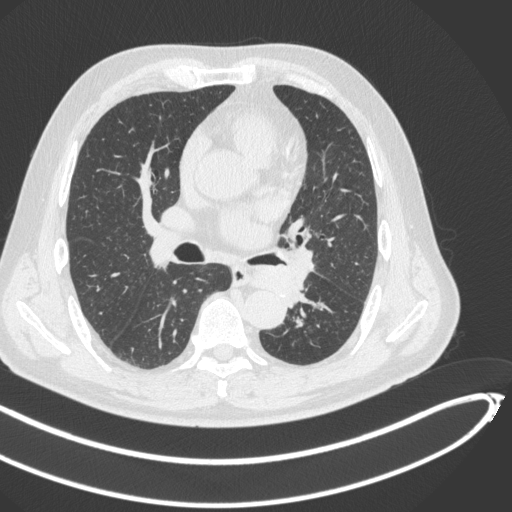
Chest CT, one axial slice; position 255 of 466 along the scan axis; reconstruction kernel B31f; 120 kVp; lung window (W 1500 / L -600 HU); 1 mm slice thickness; 512 × 512 image matrix, field of view 400 × 400 mm. Male patient, age 64 years. From the clinical record (not read from this slice): clinical TNM (as recorded): T1c N0 M0.
Annotated regions visible in this slice (bounding box drawn by a radiologist):
- lung tumour (recorded histology: squamous cell carcinoma): box from (x=251, y=262) to (x=312, y=311) px